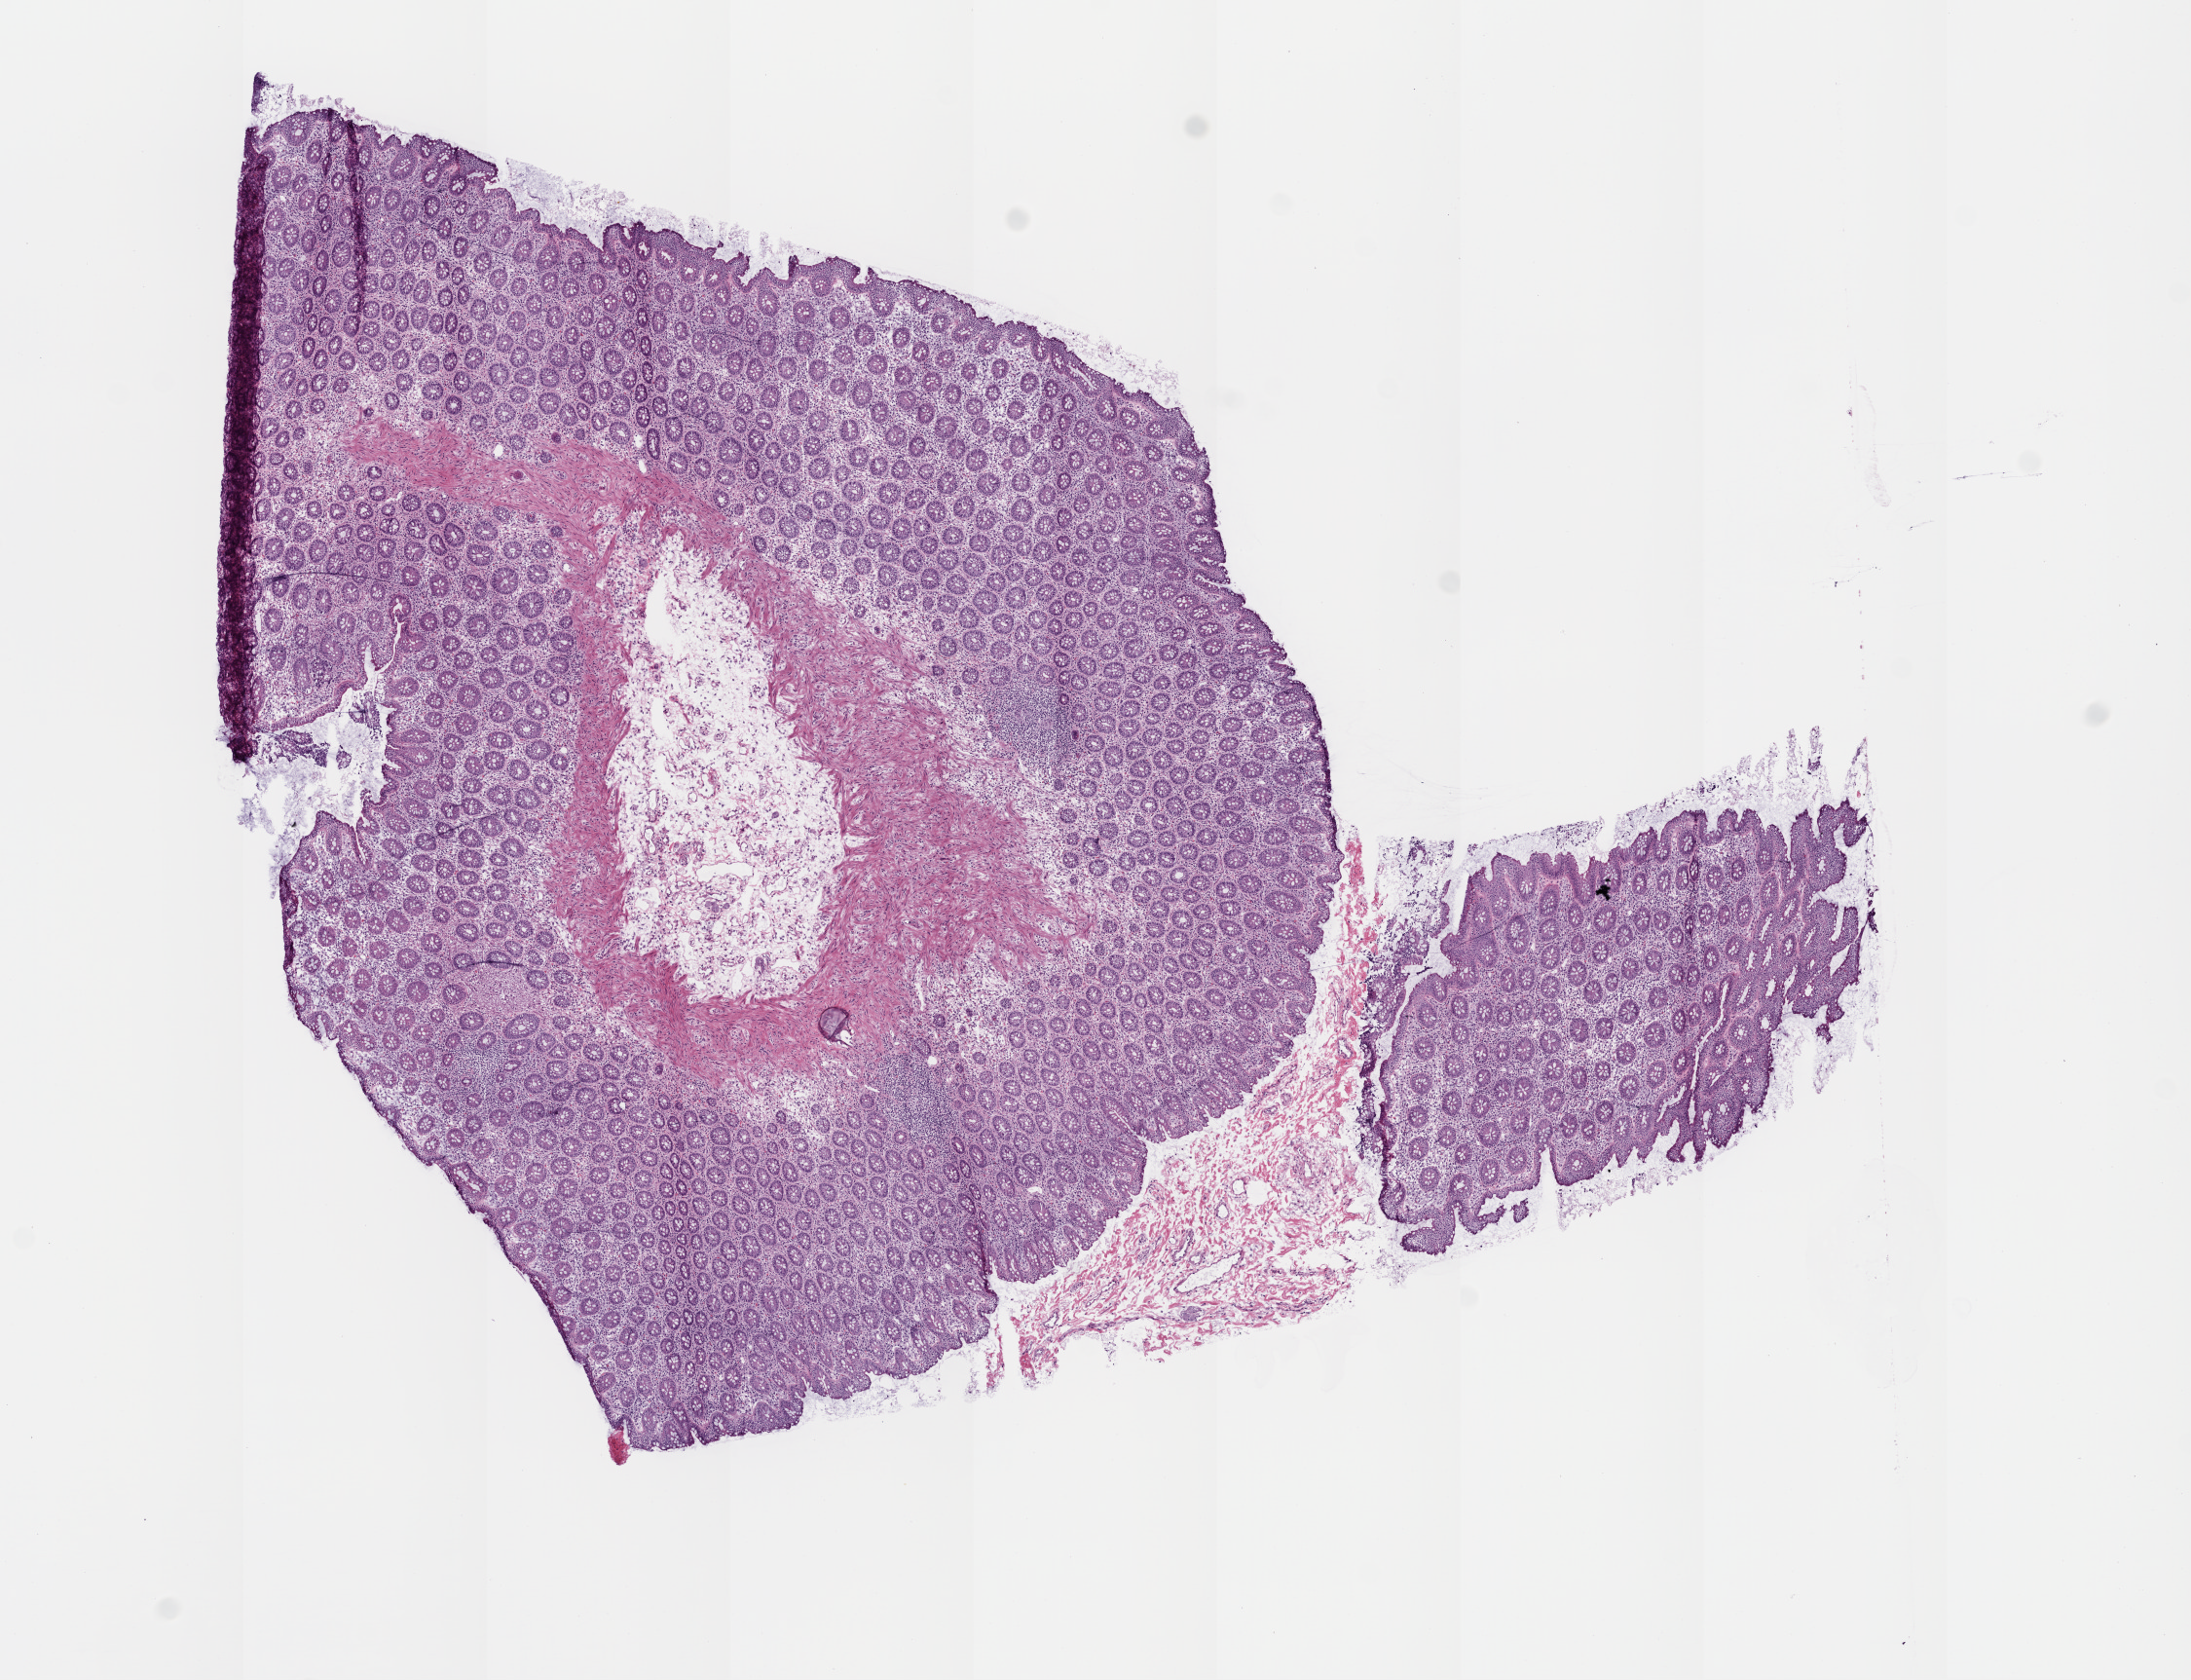
Whole-slide histology image, H&E — low-resolution overview of the scanned area, about 9.0 x 6.9 mm, frozen section, colon, solid tissue normal (non-tumour tissue) sample. Female, age 73 years at initial diagnosis.
This section: solid tissue normal sample (biorepository sample class). Patient diagnosis: Adenocarcinoma, NOS (ascending colon).